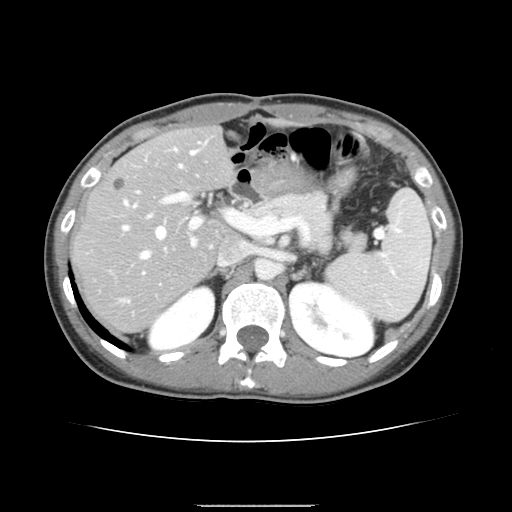
Contrast-enhanced abdominal CT, one axial slice. Position 92 of 150 along the scan axis. Intravenous contrast given. Soft-tissue window (W 400 / L 40 HU). 2.5 mm slice thickness. 512 × 512 image matrix, field of view 324 × 324 mm. Female patient, age 32 years. Case-level facts recorded for this patient, not image findings: diagnosis: colorectal cancer liver metastases, imaged before liver resection; multiple liver metastases: yes; largest metastasis: 0.7 cm; chemotherapy before resection: yes.
Outlined on this slice (outlined manually by an expert reader):
- hepatic veins: box from (x=123, y=150) to (x=197, y=258) px
- liver: (x=75, y=128)–(x=233, y=332)
- planned liver remnant (the part of the liver to remain after resection): (x=76, y=128)–(x=233, y=278)
- portal vein (with intrahepatic branches): (x=121, y=190)–(x=234, y=301)
- liver metastasis: (x=115, y=181)–(x=125, y=192)